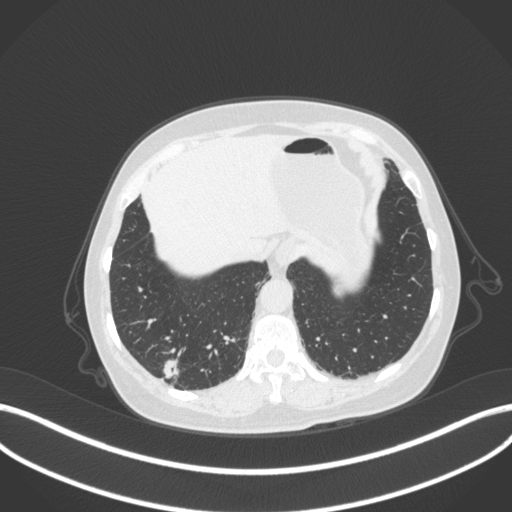
Chest CT, one axial slice. Position 52 of 340 along the scan axis. Reconstruction kernel B31f. Lung window (W 1500 / L -600 HU). 512 × 512 image matrix. Patient: female, 69 years. From the clinical record (not read from this slice): clinical TNM (as recorded): T1b N0 M0.
Annotated regions visible in this slice (bounding box drawn by a radiologist):
- lung tumour (recorded histology: adenocarcinoma): box from (x=156, y=356) to (x=182, y=382) px